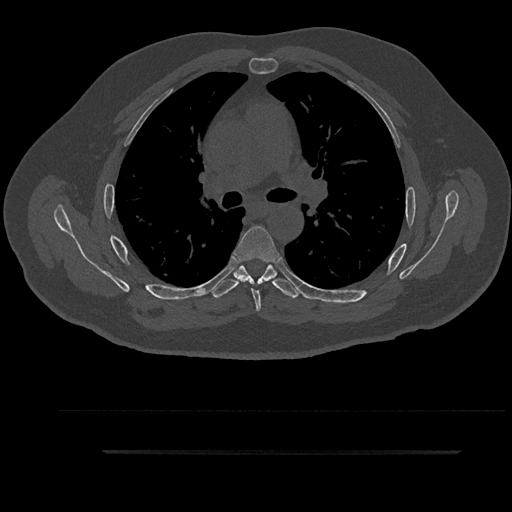
CT including the spine, one axial slice; position 605 of 797 along the scan axis; reconstruction kernel Br40s/3; bone window (W 1800 / L 400 HU); 0.5 mm slice thickness; 512 × 512 image matrix, field of view 432 × 432 mm. Male patient, age 63 years. From the clinical record (not read from this slice): primary cancer: renal.
Annotated regions visible in this slice (semi-automatically segmented with operator editing):
- T5 vertebra: bounding box <233,226,281,312> (left, top, right, bottom; pixels)
- T6 vertebra: <211,258,301,298>